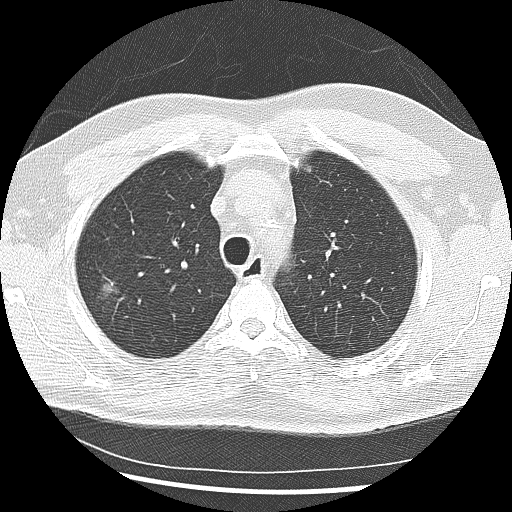
Low-dose screening chest CT, one axial slice; position 205 of 265 along the scan axis; reconstruction kernel LUNG; lung window (W 1500 / L -600 HU); 2.5 mm slice thickness; 512 × 512 image matrix, field of view 340 × 340 mm.
Outlined on this slice (outlined manually by an expert reader):
- lesion 1 (tumor, upper lobe of right lung): box from (x=102, y=283) to (x=117, y=296) px